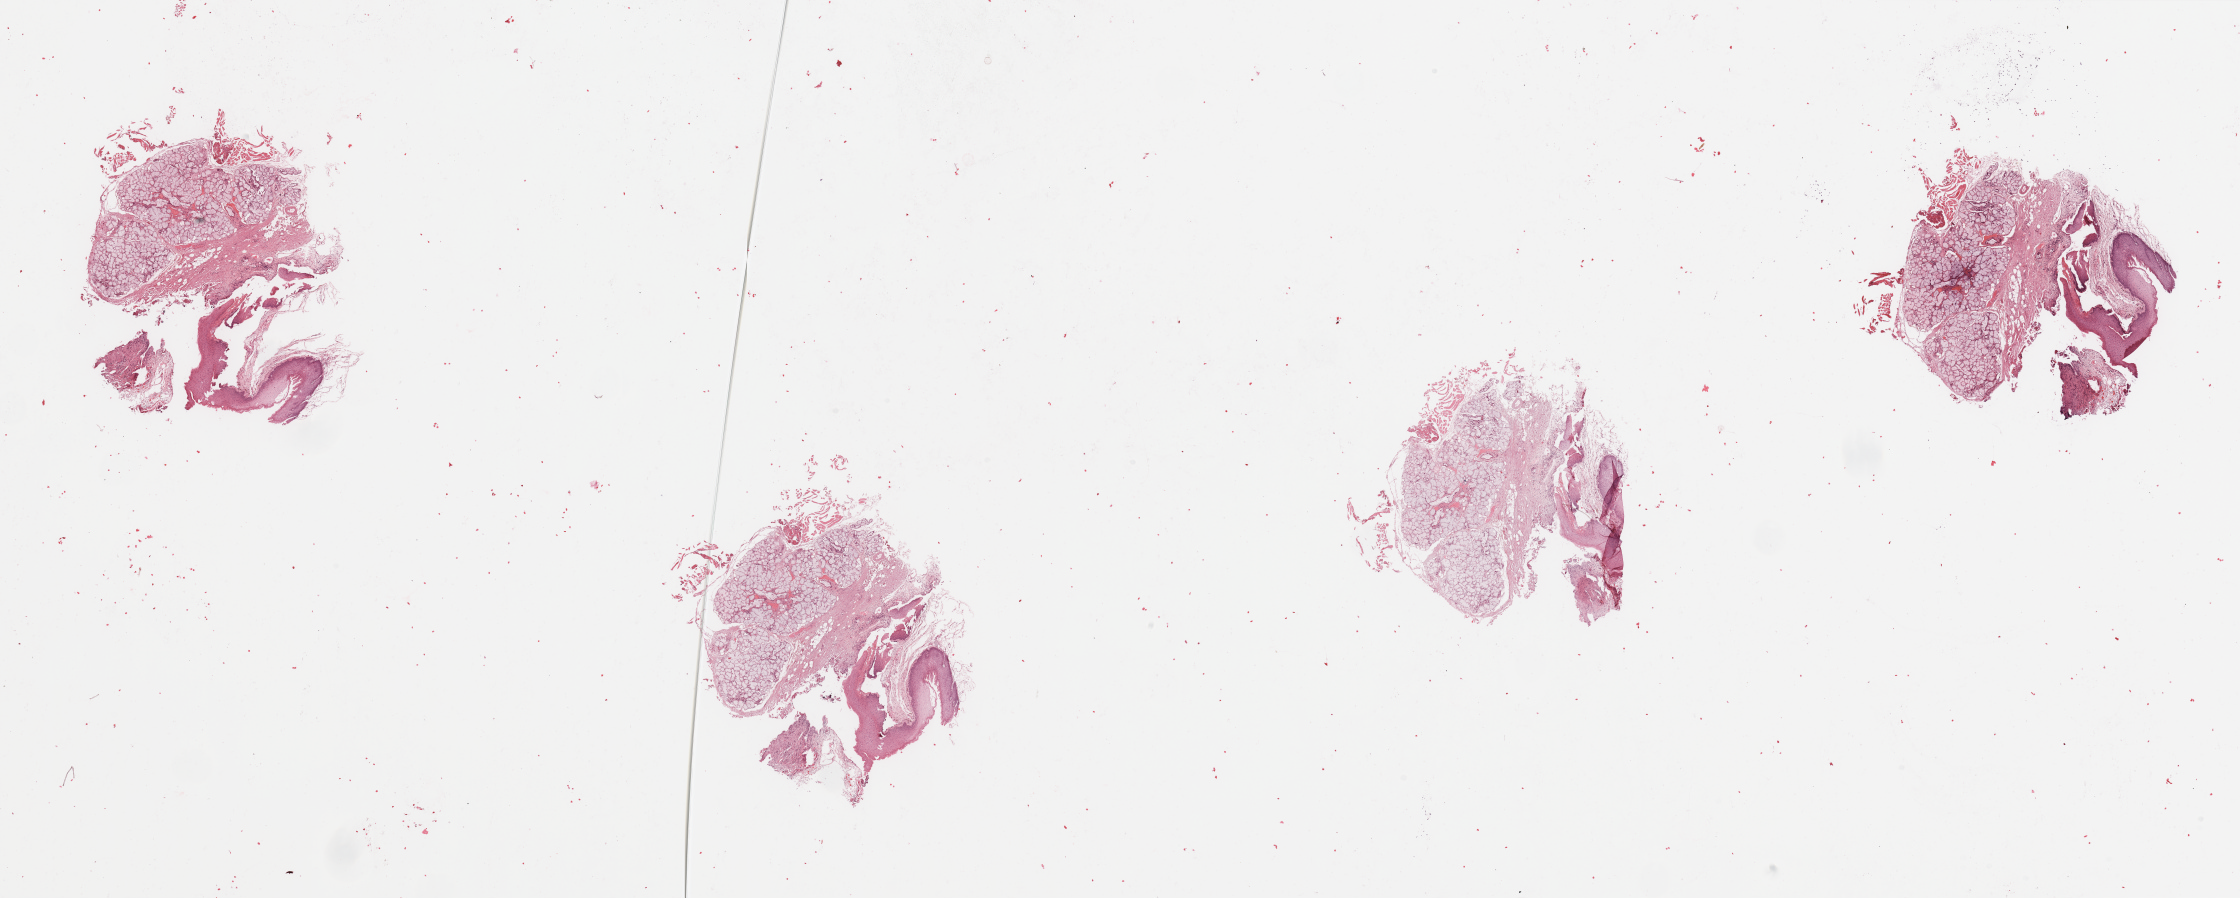
Digitized H&E tissue section (whole slide) — a low-resolution overview of the entire scanned area, about 35.4 x 14.2 mm. Head and neck, tissue type not recorded. Patient: female, age 50 years.
Patient diagnosis: Squamous cell carcinoma, NOS (floor of mouth, NOS).